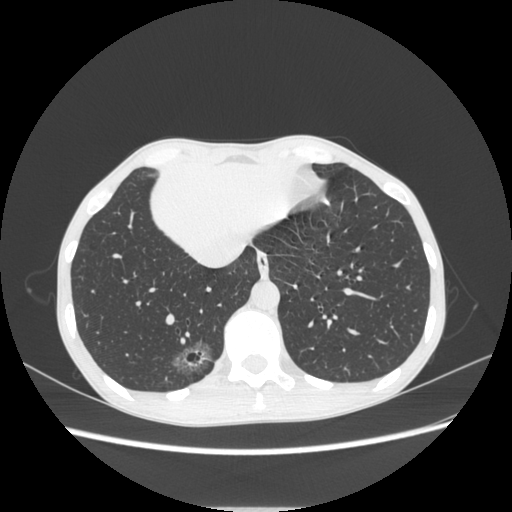
Chest CT, one axial slice; slice 74 of 272 in the series (ordered by position); 120 kVp; lung window (W 1500 / L -600 HU); 1.25 mm slice thickness; 512 × 512 image matrix, field of view 350 × 350 mm. Female patient, age 51 years. From the clinical record (not read from this slice): clinical TNM (as recorded): T1c N0 M0.
Annotated regions visible in this slice (bounding box drawn by a radiologist):
- lung tumour (recorded histology: adenocarcinoma): bounding box [x1, y1, x2, y2] px = [167, 336, 217, 381]